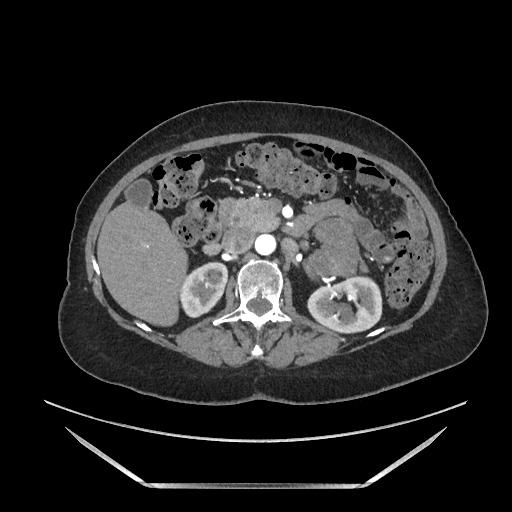
Contrast-enhanced abdominal CT, one axial slice. Slice 87 of 205 in the series (ordered by position). Soft-tissue window (W 400 / L 40 HU). 1.25 mm slice thickness. 512 × 512 image matrix, field of view 440 × 440 mm. Female patient. Case-level facts recorded for this patient, not image findings: diagnosis: adrenocortical carcinoma; tumour side: left adrenal; tumour size at pathology: 12.5 cm; Ki-67 index: 39 %; stage (as recorded): 3.
Structures marked on this image (semi-automatically segmented with operator editing):
- mass: bounding box [x1, y1, x2, y2] px = [309, 223, 368, 275]